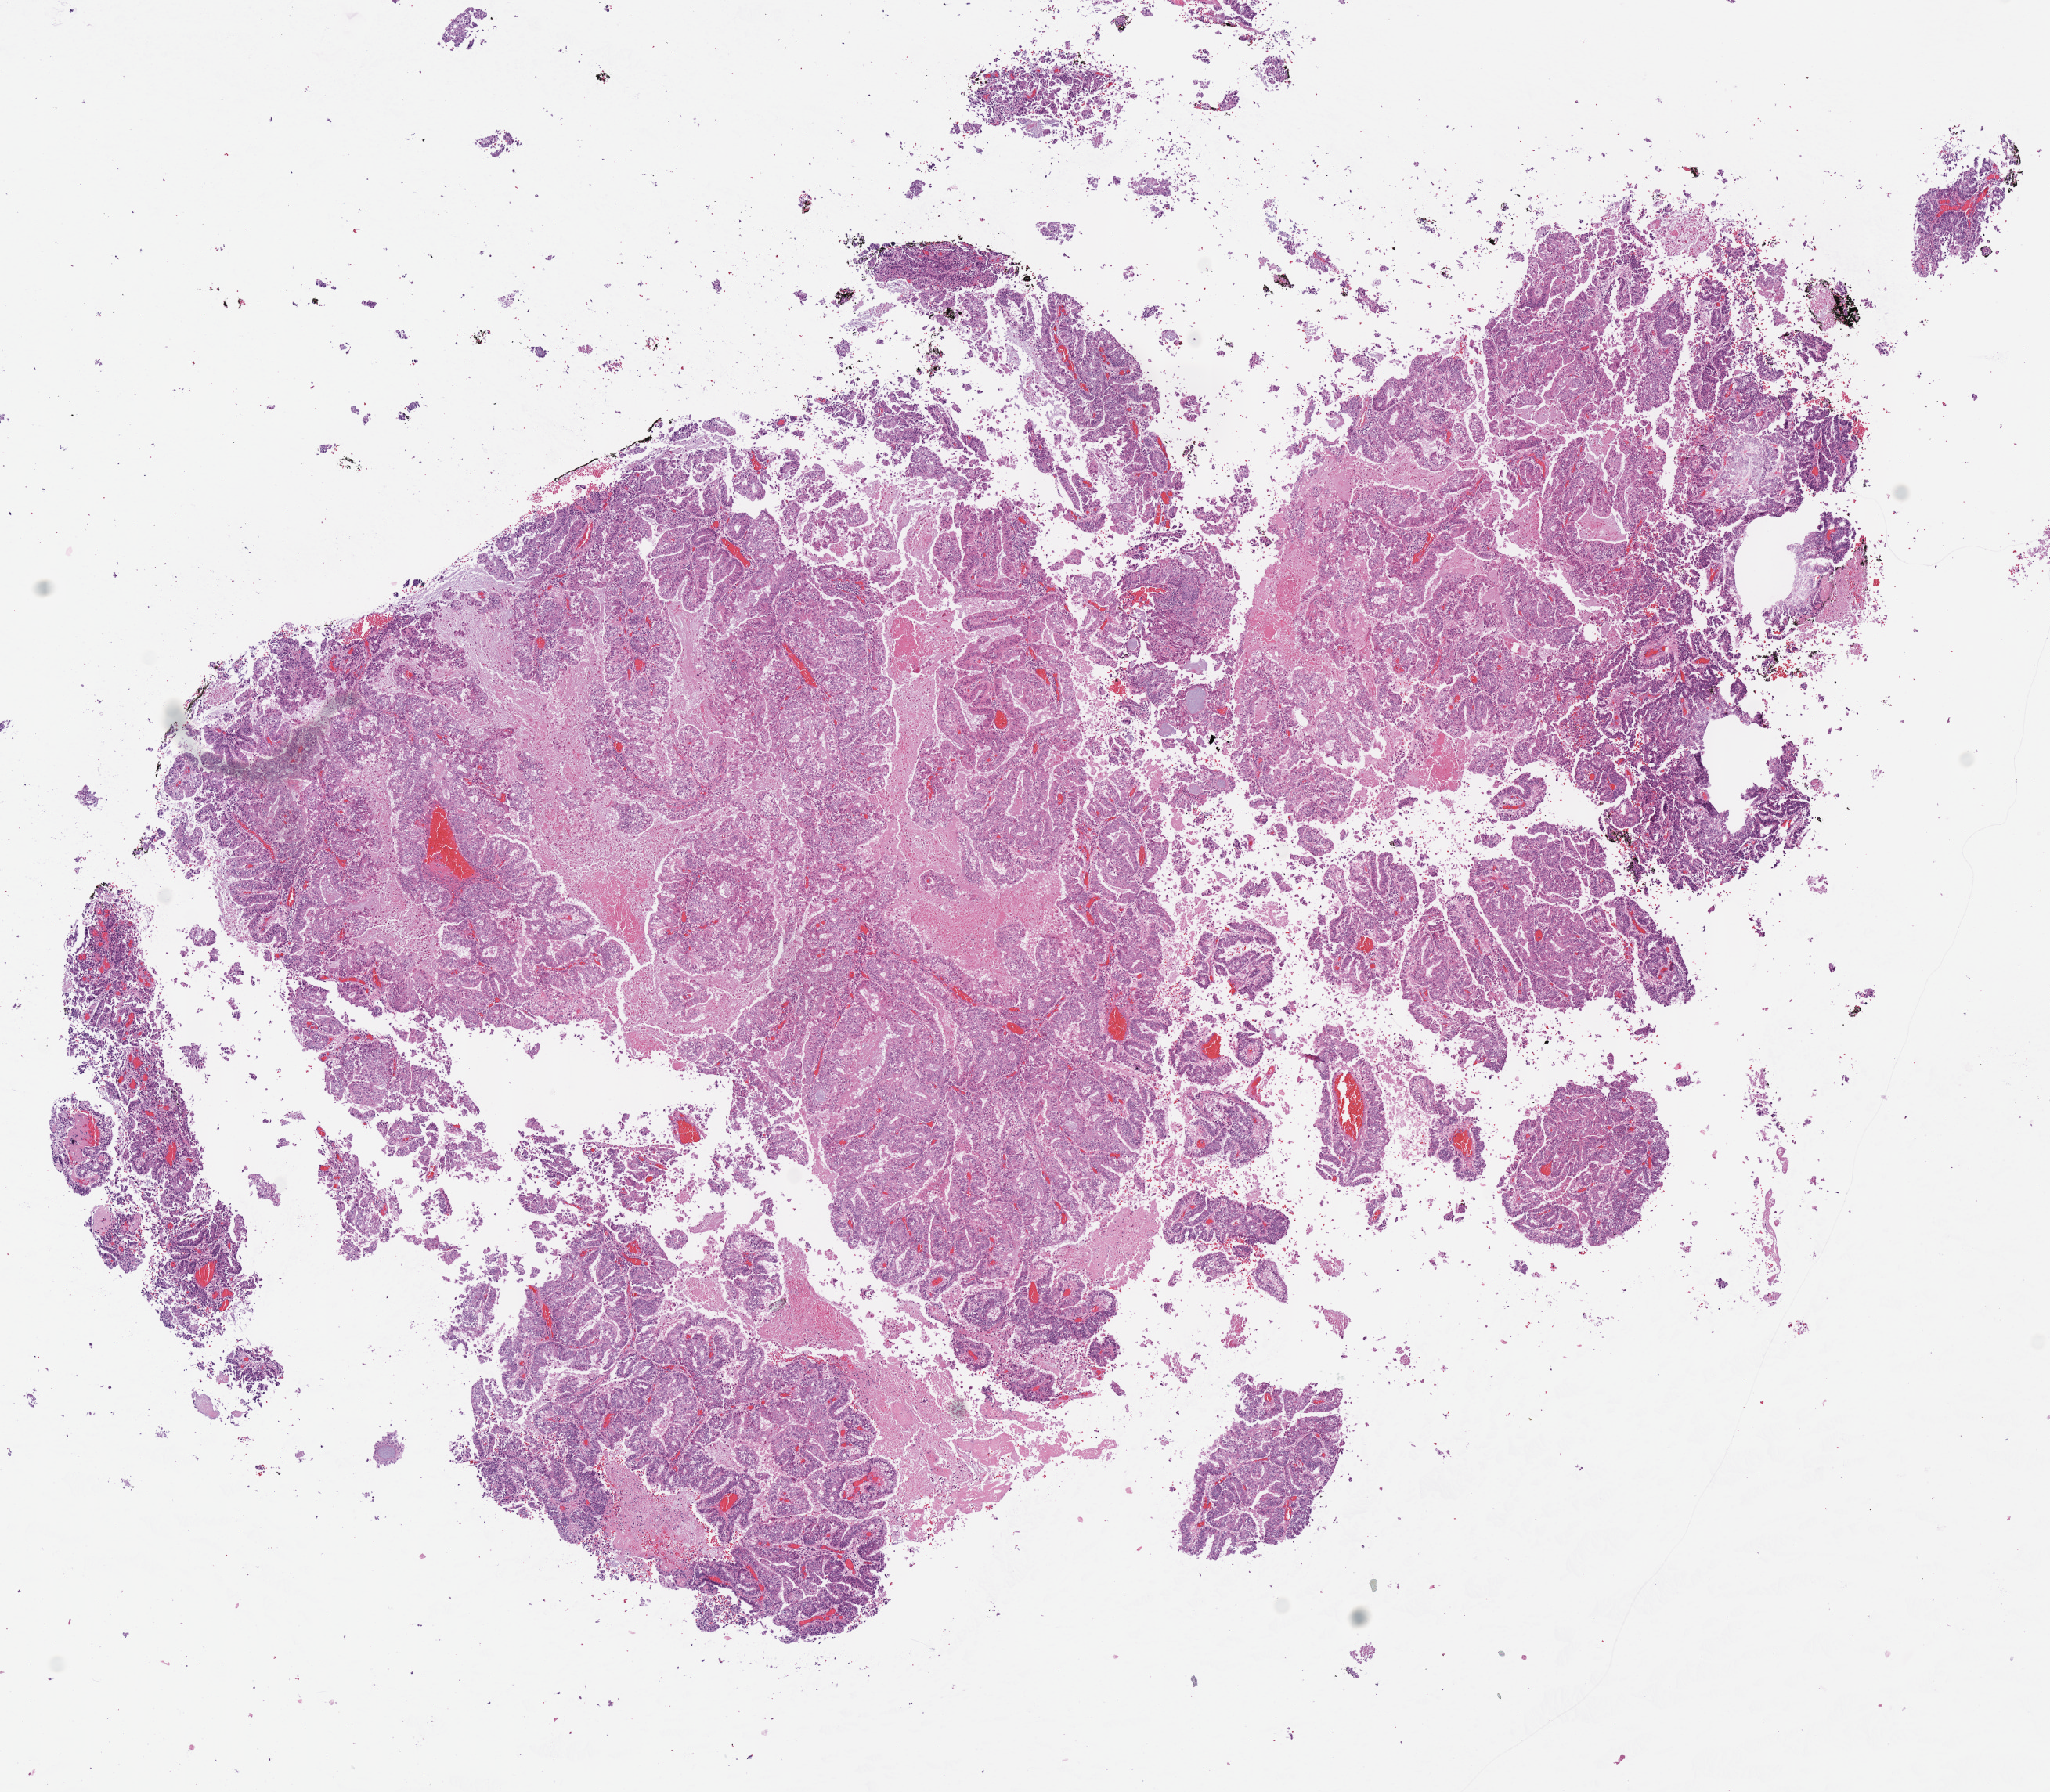
Digitized H&E-stained tissue section (whole slide) — low-resolution overview of the scanned area, about 10.3 x 9.0 mm (from a 40x scan). Formalin-fixed paraffin-embedded (FFPE) diagnostic section. Sample: primary tumour, uterus. Female patient; age at initial diagnosis 85 years. Histologic grade: G3 (poorly differentiated).
- FIGO stage: IB
- histologic diagnosis: Endometrioid adenocarcinoma, NOS (endometrium)